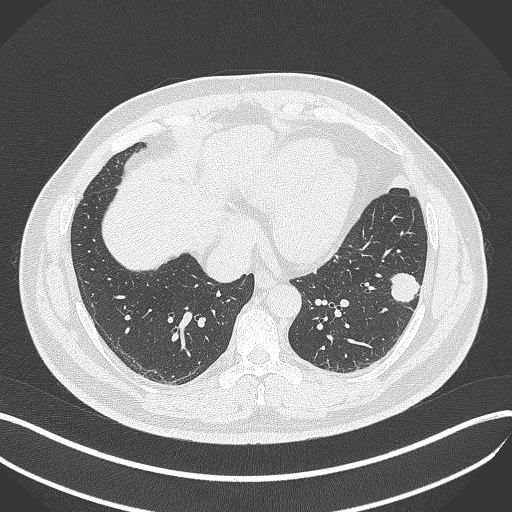
Chest CT, one axial slice. Position 140 of 429 along the scan axis. Reconstruction kernel B70f. 120 kVp. Lung window (W 1500 / L -600 HU). 1 mm slice thickness. 512 × 512 image matrix. Patient: male, 39 years. From the clinical record (not read from this slice): clinical TNM (as recorded): T2a N0 M0.
Structures marked on this image (rectangle marked by the reading radiologist):
- lung tumour (recorded histology: adenocarcinoma): bounding box [x1, y1, x2, y2] px = [382, 268, 423, 307]